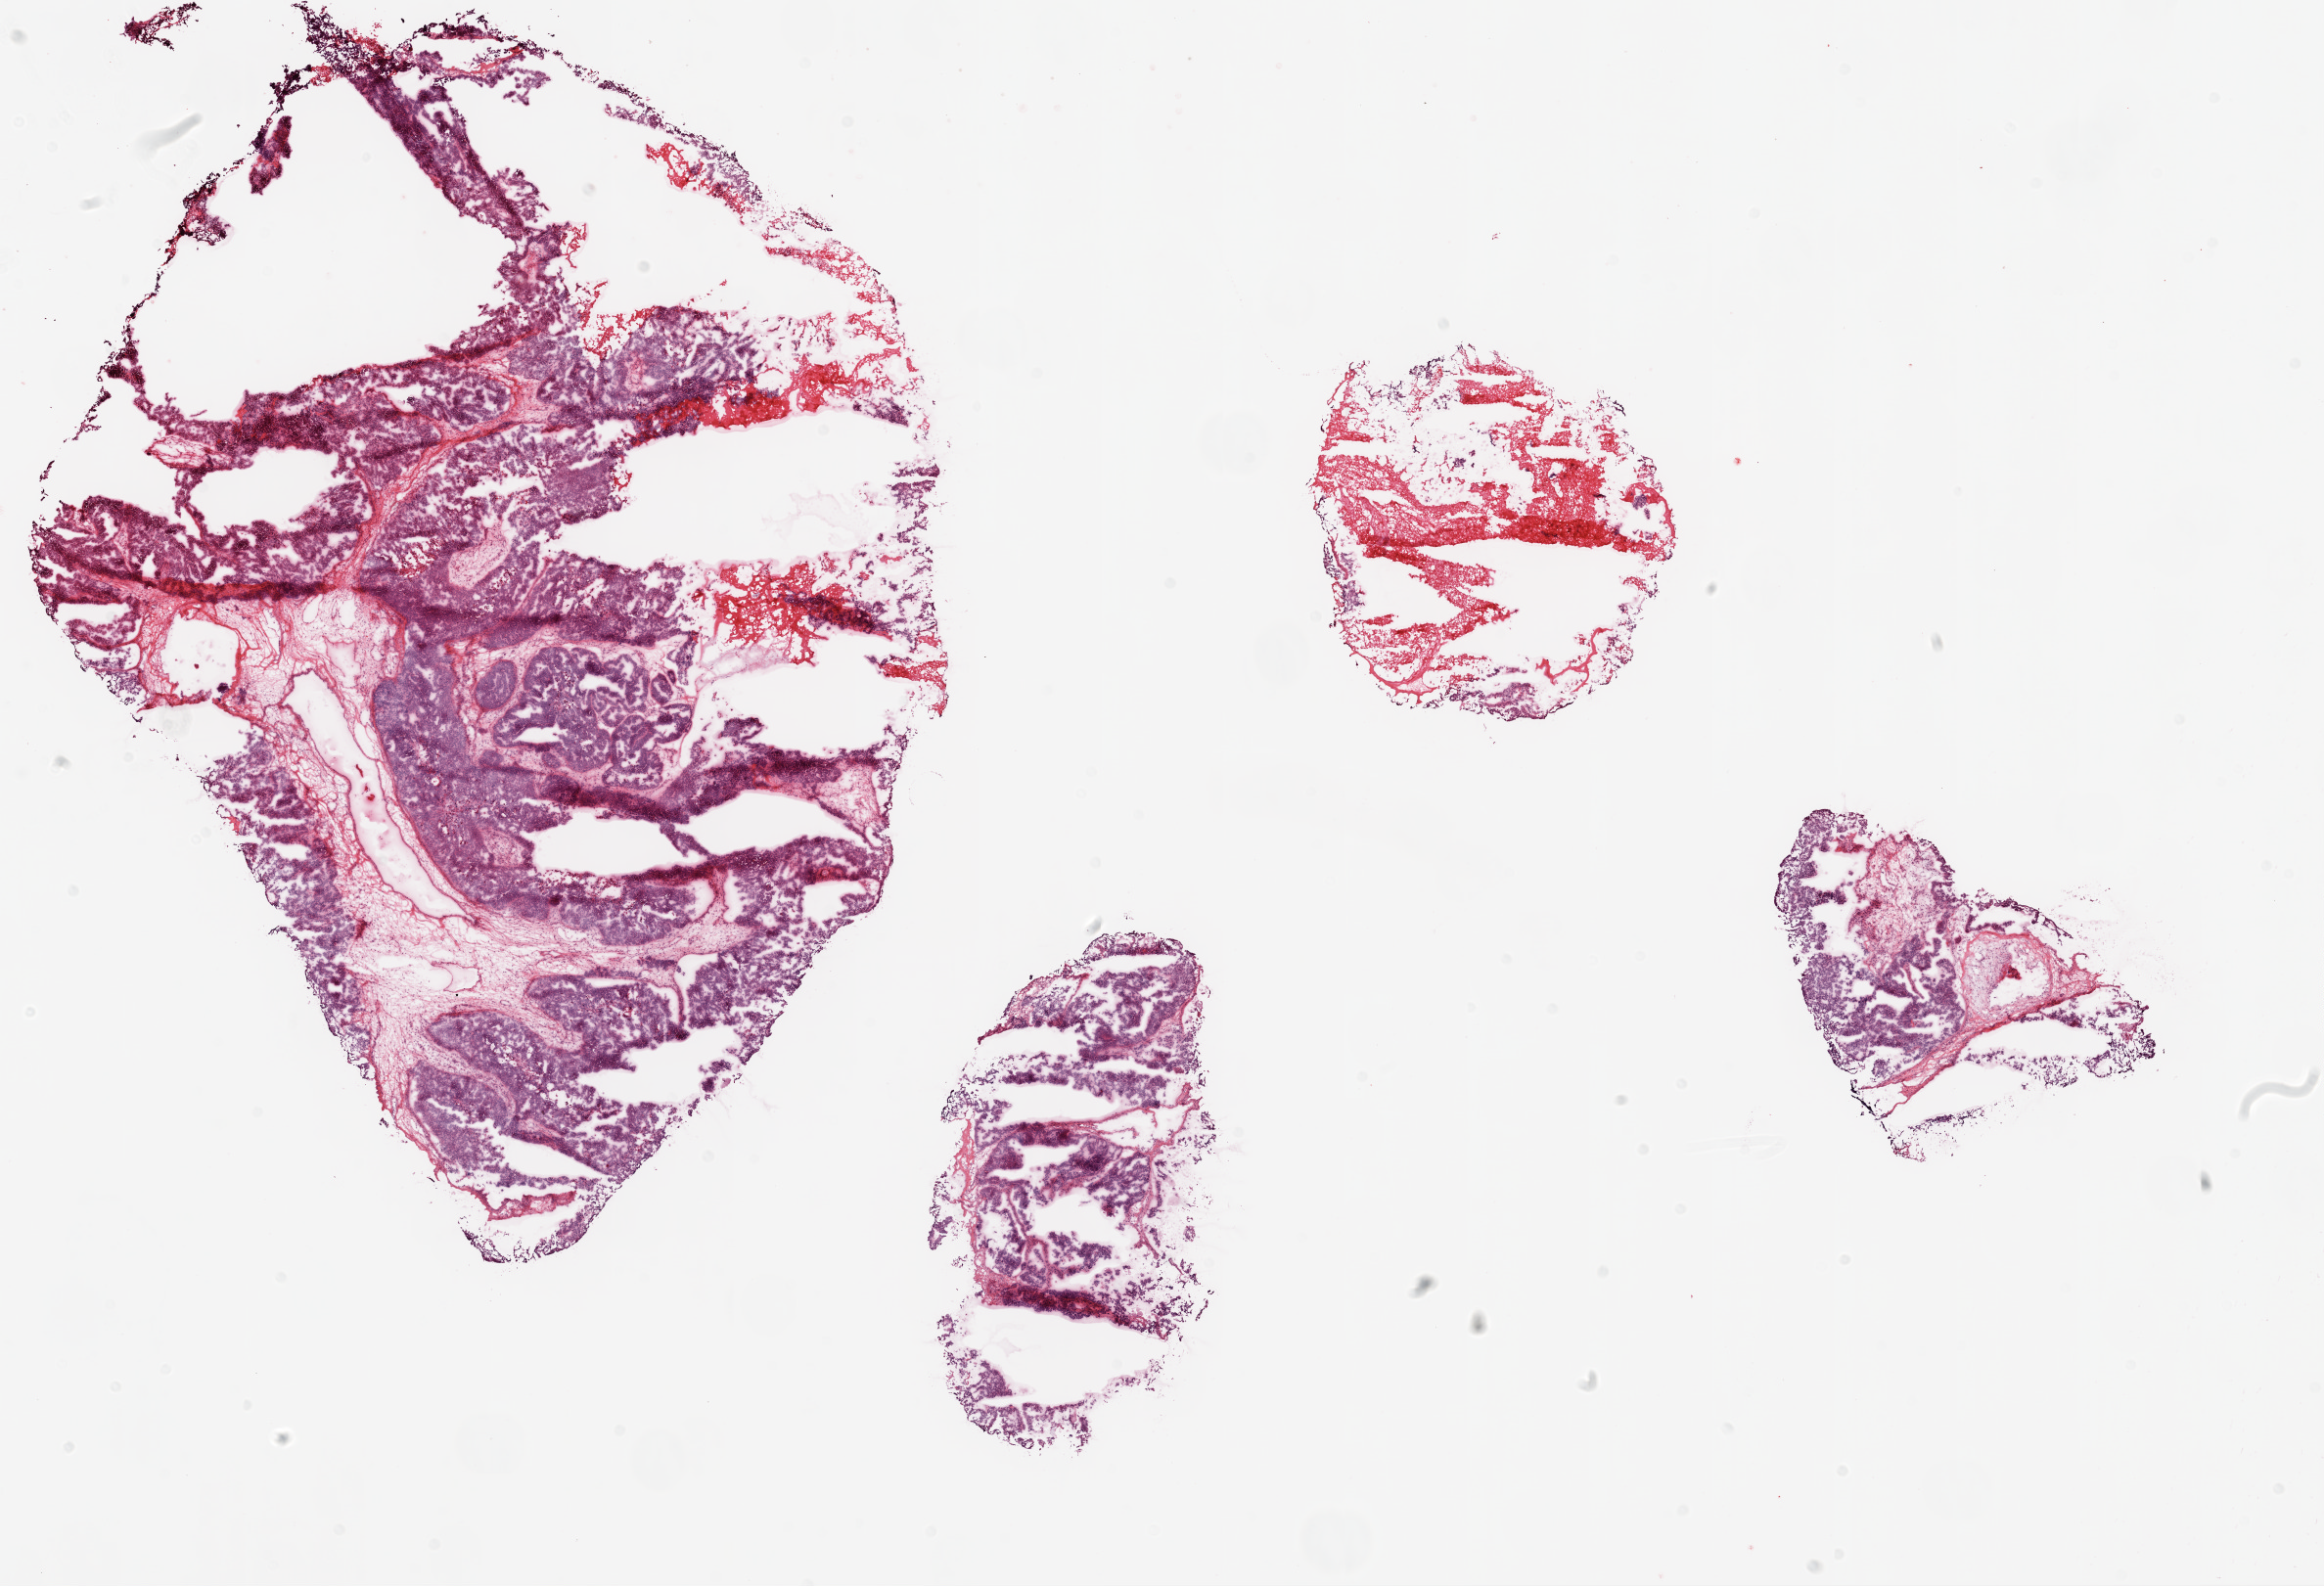
Digitized H&E tissue section (whole slide), low-resolution overview of the scanned area, about 19.1 x 13.0 mm (from a 20x scan), frozen section from the top of the tissue portion, primary tumour sample from the ovary. Female, age 70 years at initial diagnosis. Histologic grade: G3 (poorly differentiated). Pathologist review of this section (percent, as recorded): tumour cells 70%, tumour nuclei 70%, normal cells 0%, stromal cells 30%, necrosis 0%. Infiltration values recorded for this section: lymphocyte infiltration 0%, monocyte infiltration 0%, neutrophil infiltration 0%.
Histologic diagnosis: Serous cystadenocarcinoma, NOS. FIGO stage: IIIC. Laterality: bilateral.